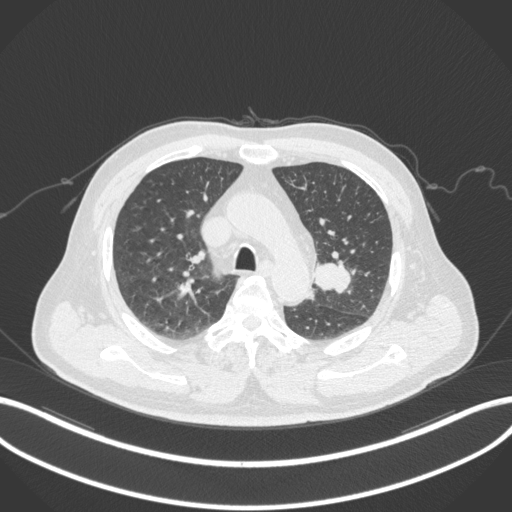
Chest CT, one axial slice. Reconstruction kernel B31f. 120 kVp. Lung window (W 1500 / L -600 HU). 1 mm slice thickness. 512 × 512 image matrix, field of view 400 × 400 mm. Male patient, age 67 years. Case-level facts recorded for this patient, not image findings: clinical TNM (as recorded): T2a N1 M0.
Annotated regions visible in this slice (bounding box drawn by a radiologist):
- lung tumour (recorded histology: adenocarcinoma): bounding box [x1, y1, x2, y2] px = [311, 256, 353, 294]